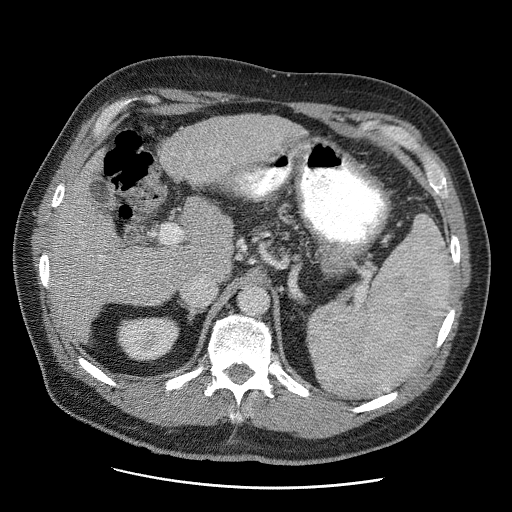
Contrast-enhanced abdominal CT (liver protocol), one axial slice; position 28 of 81 along the scan axis; reconstruction kernel STANDARD; soft-tissue window (W 400 / L 40 HU); 512 × 512 image matrix, field of view 380 × 380 mm. Case-level facts recorded for this patient, not image findings: diagnosis: hepatocellular carcinoma (patient treated with transarterial chemoembolisation; whether this scan precedes or follows treatment is not stated here); TNM stage (as recorded): Stage-IIIA; Child-Pugh class: A; tumour differentiation: moderately differentiated.
Structures marked on this image (semi-automatic segmentation, software-assisted and operator-edited):
- abdominal aorta: bounding box <239,287,268,316> (left, top, right, bottom; pixels)
- liver parenchyma outside the tumour (the mass and vessels are separate outlines, so this box may not span the whole liver): <50,114,304,338>